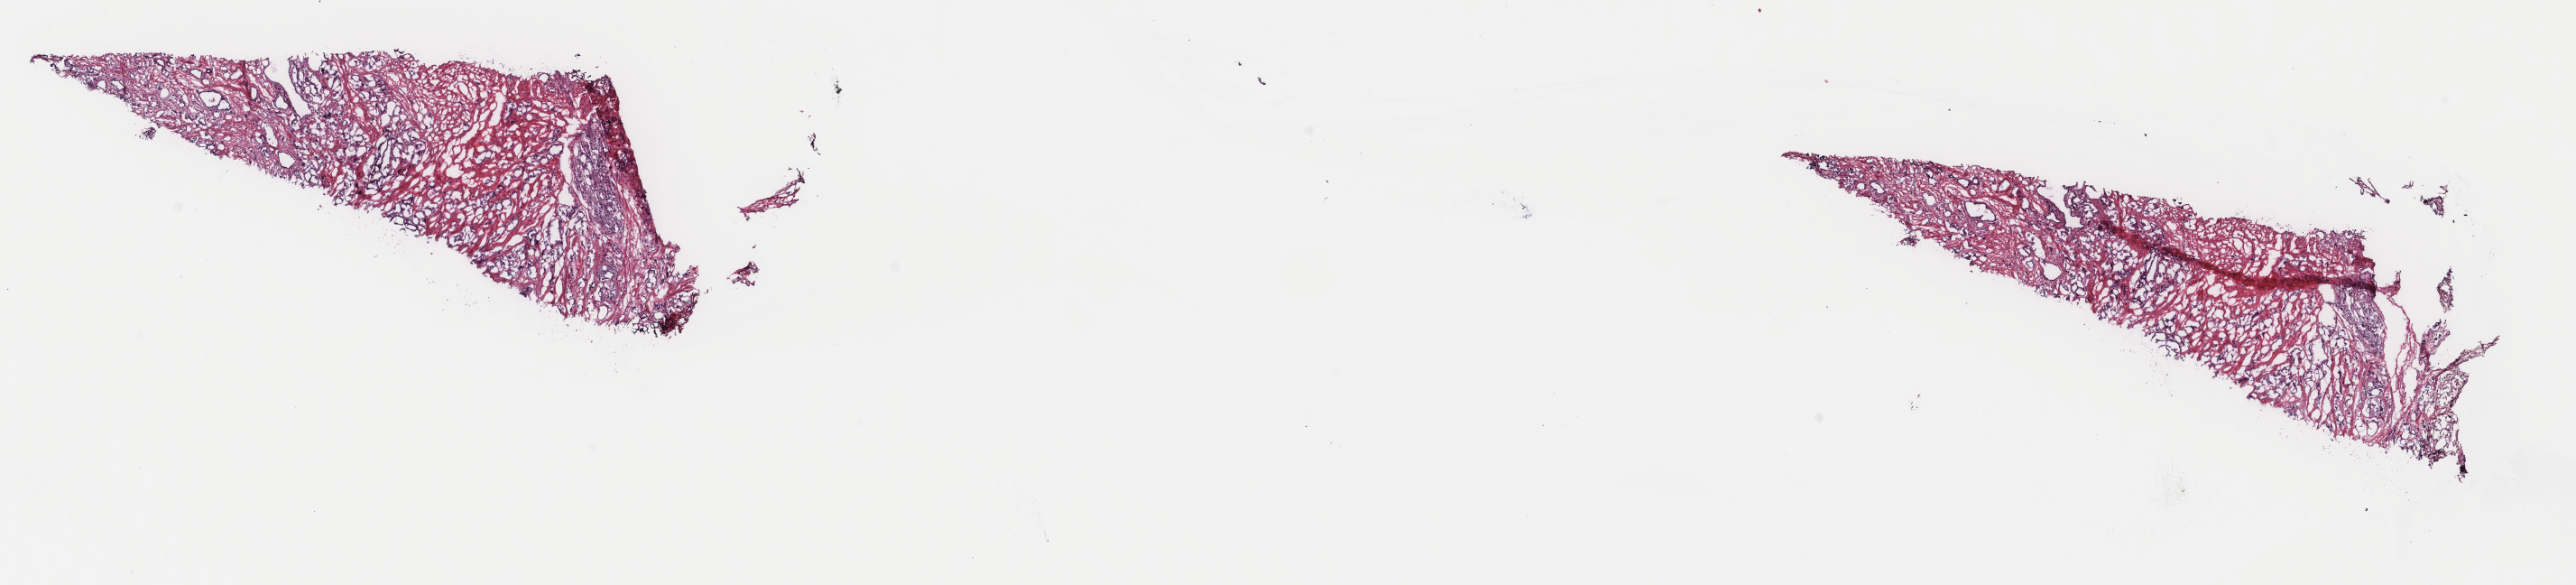
H&E-stained whole-slide image, whole scanned area (about 22.7 x 5.1 mm, slide scanned at 40x) shown as a low-resolution overview; frozen section from the top of the tissue portion; prostate, primary tumour sample. Male, age 46 years at initial diagnosis. Gleason score: 9 (5+4). Slide review estimates, as recorded: tumour cells 100%, tumour nuclei 60%, normal cells 0%, stromal cells 0%, necrosis 0%. Infiltration values recorded for this section: lymphocyte infiltration 1%, monocyte infiltration 0%, neutrophil infiltration 0%.
Laterality: bilateral. Lymph nodes positive (case pathology): 1 of 11 examined. Histologic diagnosis: Adenocarcinoma, NOS (prostate gland).